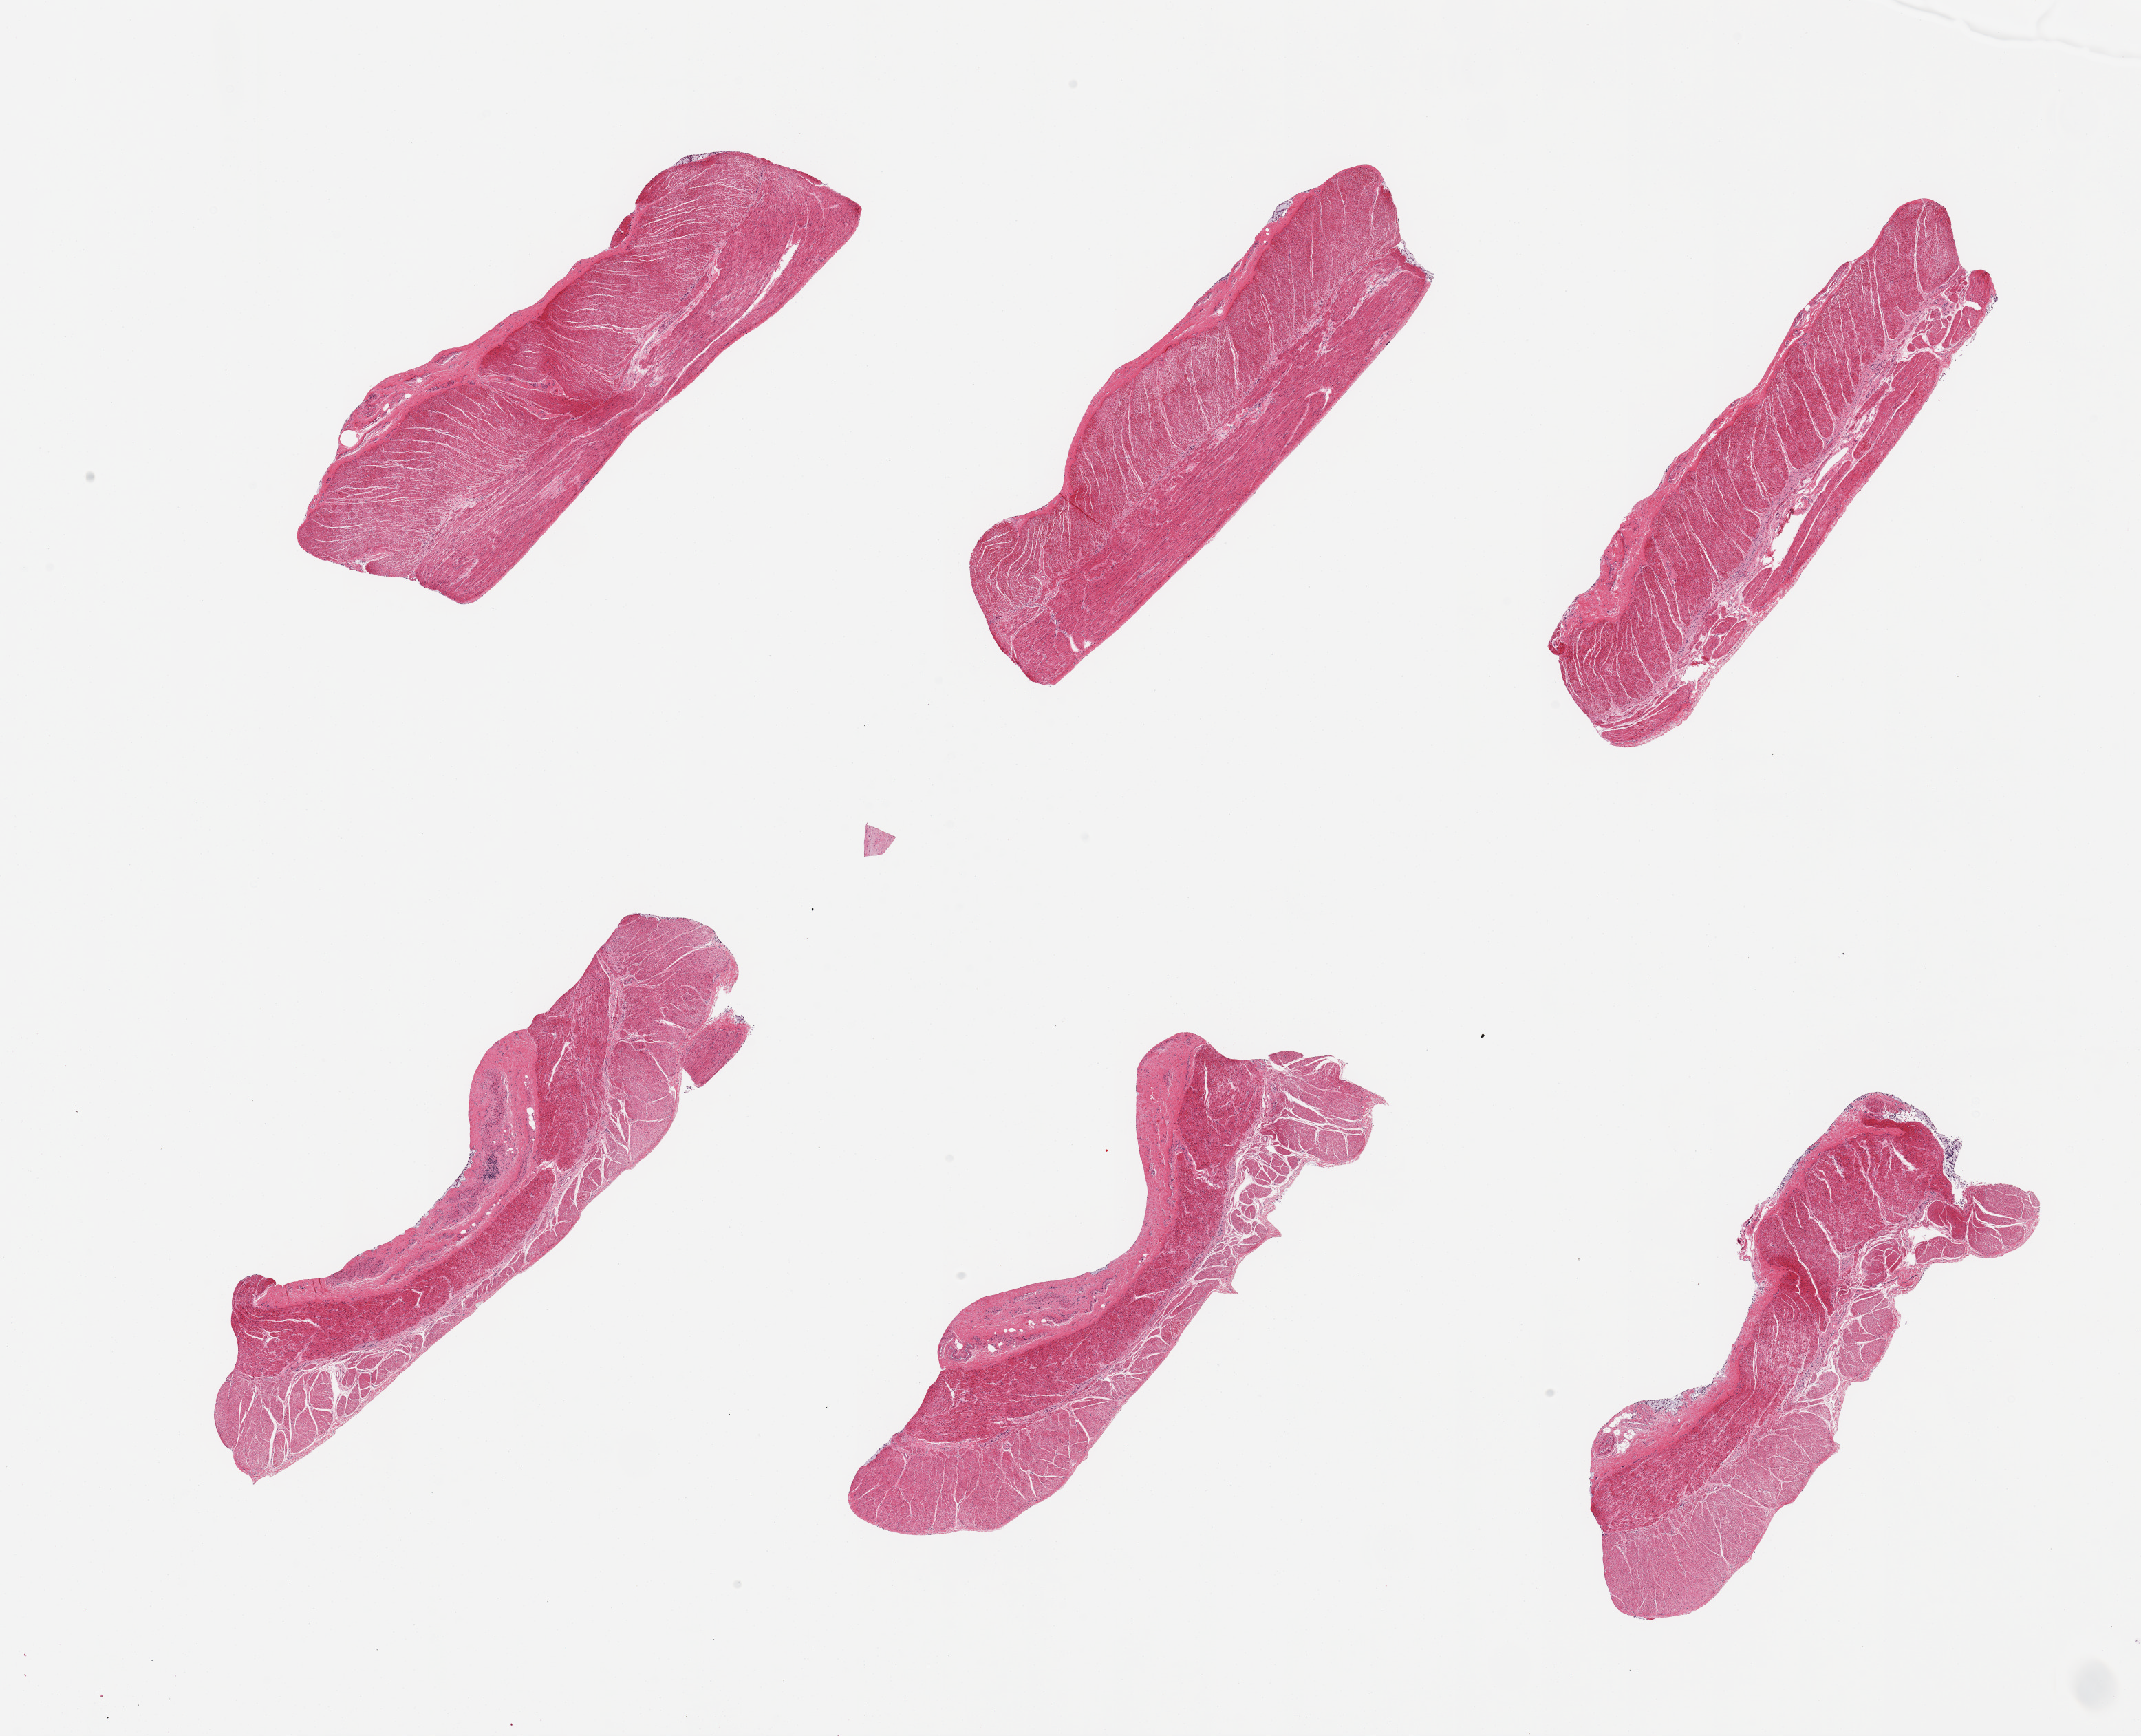
Whole-slide image, haematoxylin and eosin stain — low-resolution overview of the scanned area, about 24.6 x 20.0 mm. PAXgene-fixed paraffin-embedded (PFPE) section. Section of sigmoid colon (target tissue). Donor tissue sample. Donor sex: male.
- pathologist's review note for this sample: 6 pieces, confirmed target muscularis